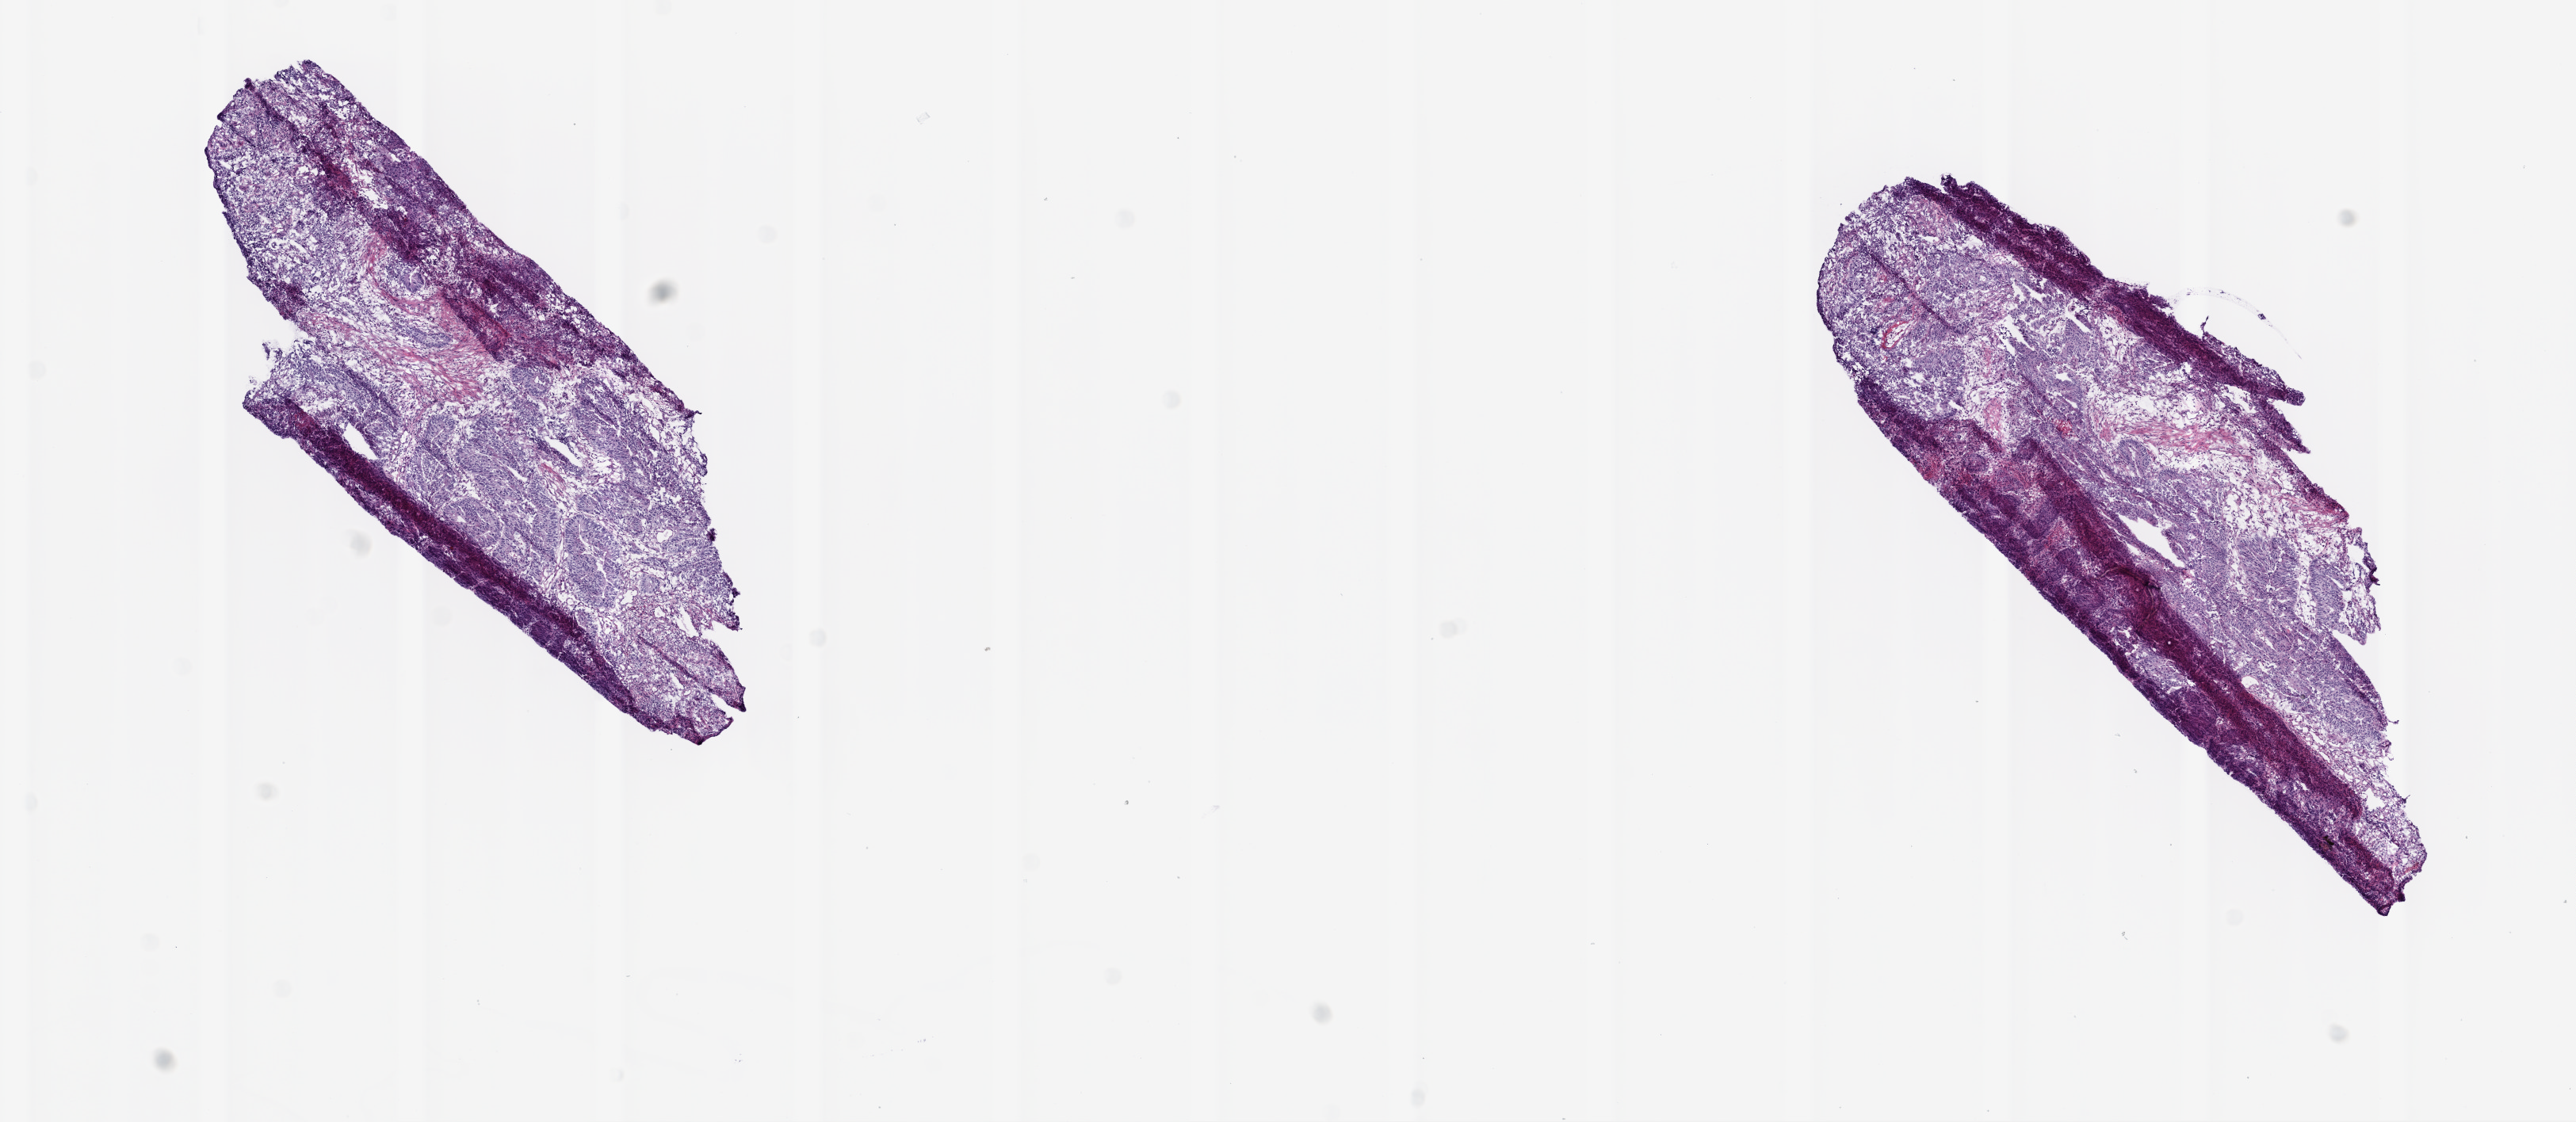
Hematoxylin and eosin (H&E) stained whole-slide image — whole scanned area (about 13.0 x 5.7 mm, slide scanned at 20x) shown as a low-resolution overview, frozen section from the top of the tissue portion, sample: primary tumour, colon. Patient: male, age at initial diagnosis 58 years. Pathologist review of this section (percent, as recorded): tumour cells 93%, tumour nuclei 75%.
Histologic diagnosis: Adenocarcinoma, NOS (rectosigmoid junction).